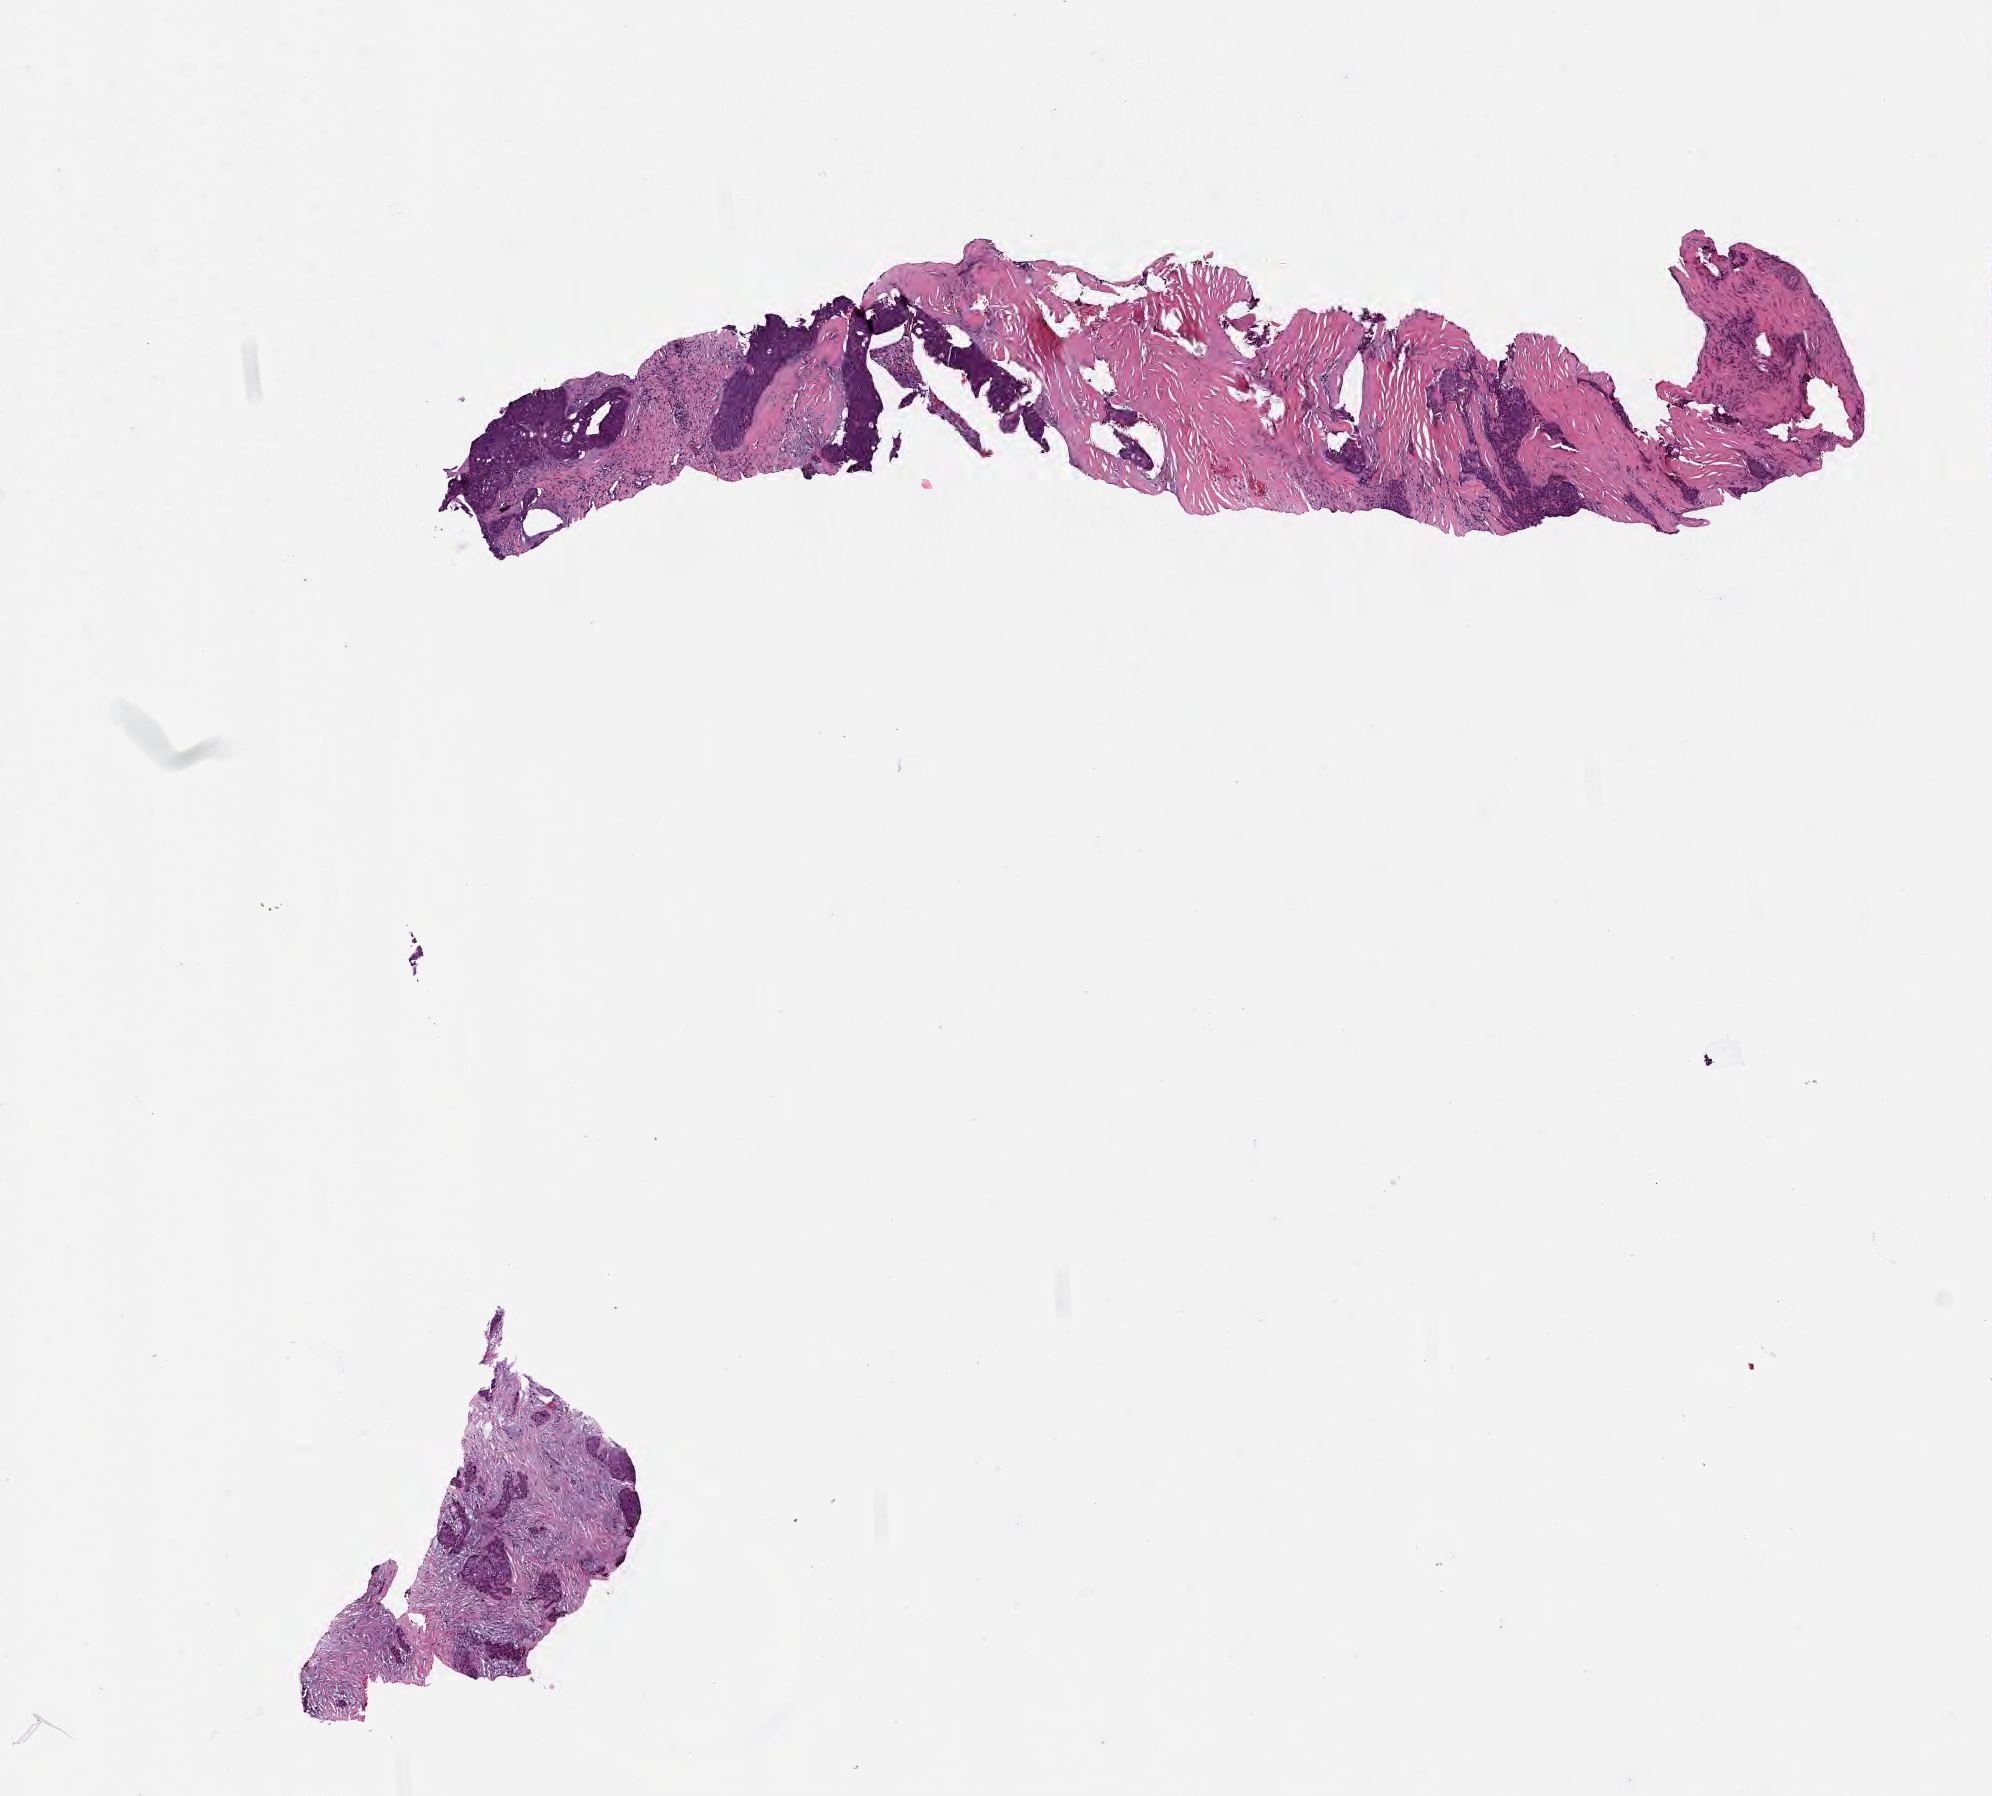
Haematoxylin and eosin whole-slide image, whole scanned area (about 8.0 x 7.3 mm) shown as a low-resolution overview; tumor tissue; site: lung. Female patient, aged 68.
Diagnosis: Squamous cell carcinoma, large cell, nonkeratinizing, NOS.